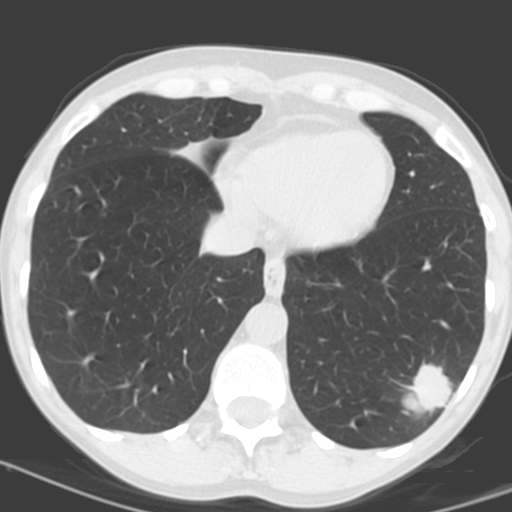
Chest CT (low-dose screening protocol), one axial image, baseline annual screen, lung window (W 1500 / L -600 HU), 3.2 mm slice thickness, standard (soft-tissue) reconstruction kernel (C), slice 112 of 156 in the series, 512 × 512 image matrix. Female, age 56 years at enrolment. Current smoker at enrolment.
Expert reader's lesion annotation, bounding box <391,356,467,424> (left, top, right, bottom; pixels). Reader record for this screening exam (exam-level; its link to the box is not recorded): non-calcified nodule or mass ≥4 mm, left lower lobe, 31 × 23 mm, poorly defined margins, soft tissue attenuation, pre-existing on the prior screen: no. Participant outcome: lung cancer diagnosed 27 days after this screen — squamous cell carcinoma, NOS, left lower lobe, poorly differentiated (G3), stage IB (AJCC 6th edition), 35 mm at pathology.